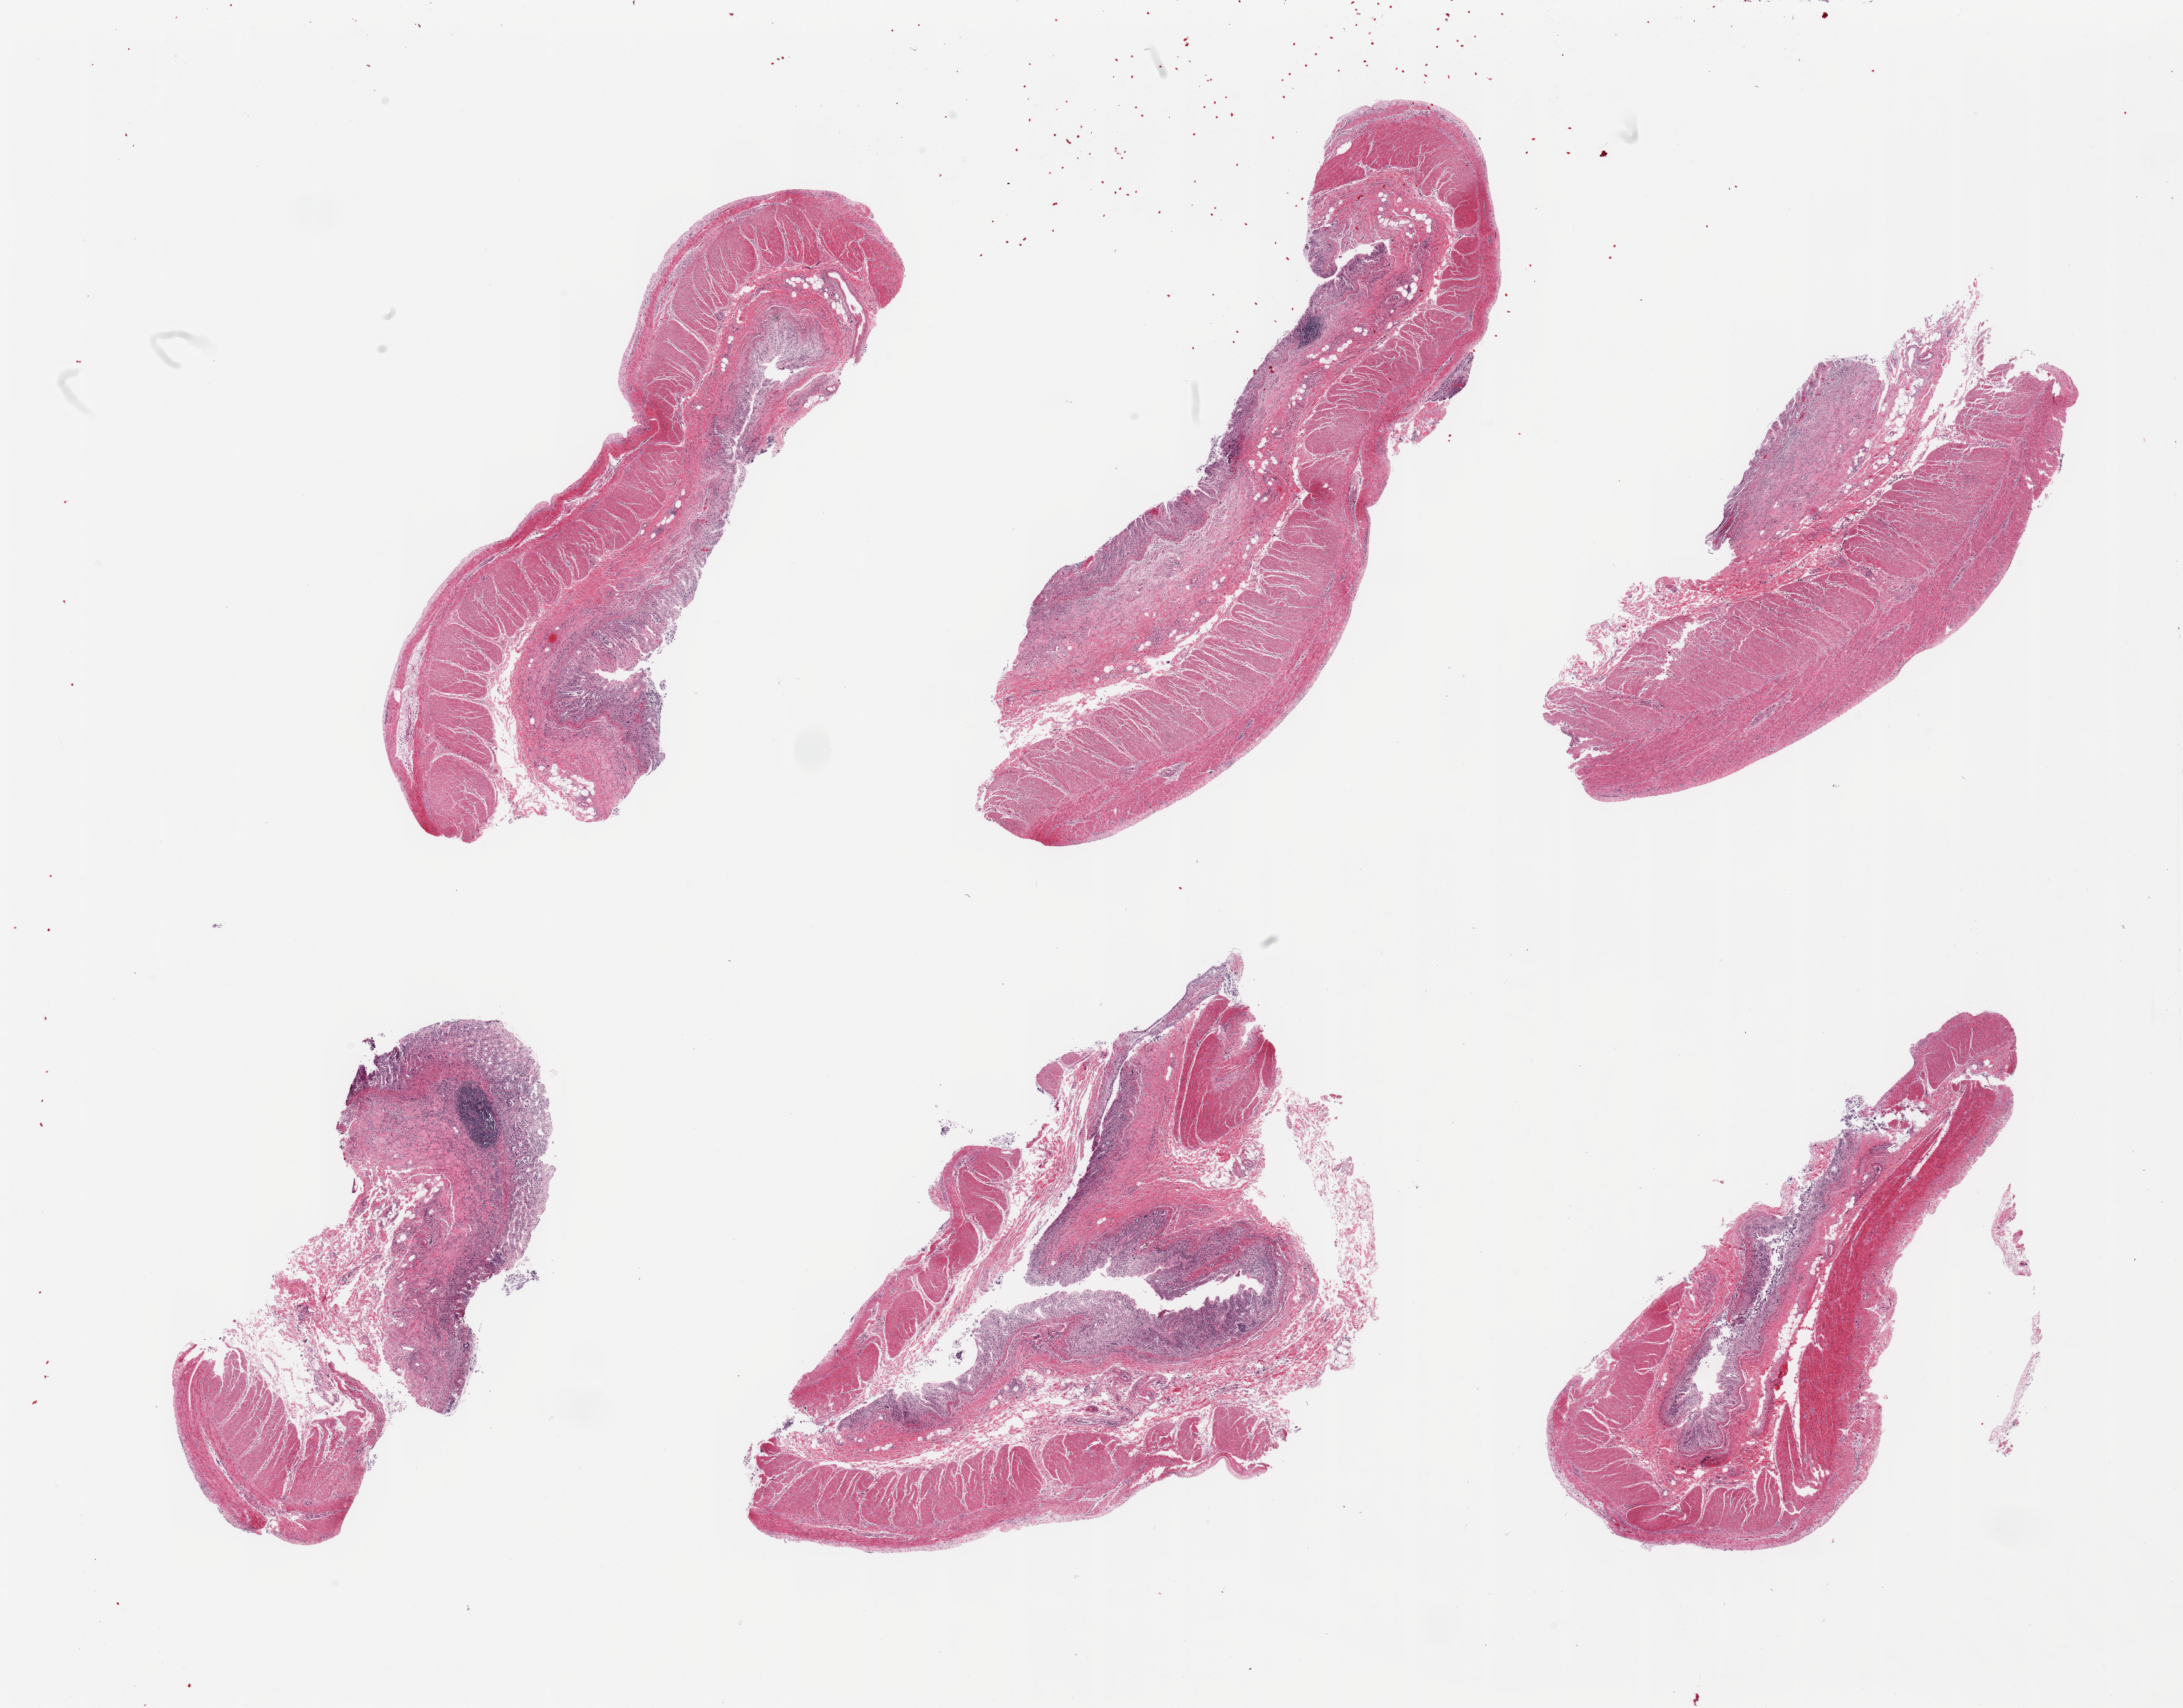
Whole-slide image, hematoxylin and eosin (H&E) stain, brightfield — a low-resolution overview of the entire scanned area, about 27.6 x 21.6 mm (from a 20x scan). PAXgene-fixed, paraffin-embedded tissue. Sampled site (target tissue): transverse colon. Donor tissue sample. Female donor.
Review note (as recorded): 6 pieces, mucosa up to ~0.3mm, advanced autolysis.